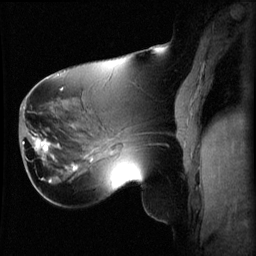
Breast MRI (dynamic contrast-enhanced), one sagittal slice. Position 26 of 60 along the scan axis. 3 images stored at this slice position (order not interpretable as contrast timing). 1.5 T. TE 4.2 ms, TR 8.2 ms. 2.2 mm slice thickness. 256 × 256 image matrix, field of view 220 × 220 mm. Female patient, age 62 years.
Annotated regions visible in this slice (semi-automatic segmentation, software-assisted and operator-edited):
- analysis volume of interest (the breast-tissue region the enhancement analysis was run in; not a lesion): bounding box <26,126,59,165> (left, top, right, bottom; pixels)
- tumour enhancement mask (voxels above the 70 % enhancement threshold inside the analysis volume of interest): <32,134,55,159>